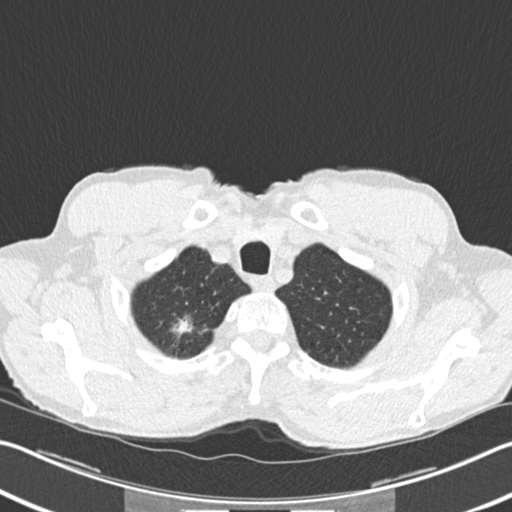
Chest CT (low-dose screening protocol), one axial image. Second annual screen. Lung window (W 1500 / L -600 HU). 2 mm slice thickness. Male, age 62 years at enrolment. Former smoker at enrolment.
Expert reader's lesion annotation, box from (x=161, y=306) to (x=206, y=349) px. The screening reader recorded 2 non-calcified nodules or masses ≥4 mm on this exam; which of them this box marks is not recorded. Official screen result: positive, change unspecified: nodule(s) >= 4 mm or enlarging nodule(s), mass(es), or other non-specific abnormalities suspicious for lung cancer. Participant outcome: lung cancer diagnosed 5 days after this screen — bronchiolo-alveolar adenocarcinoma, NOS, right upper lobe, well differentiated (G1), stage IA (AJCC 6th edition), 15 mm at pathology.